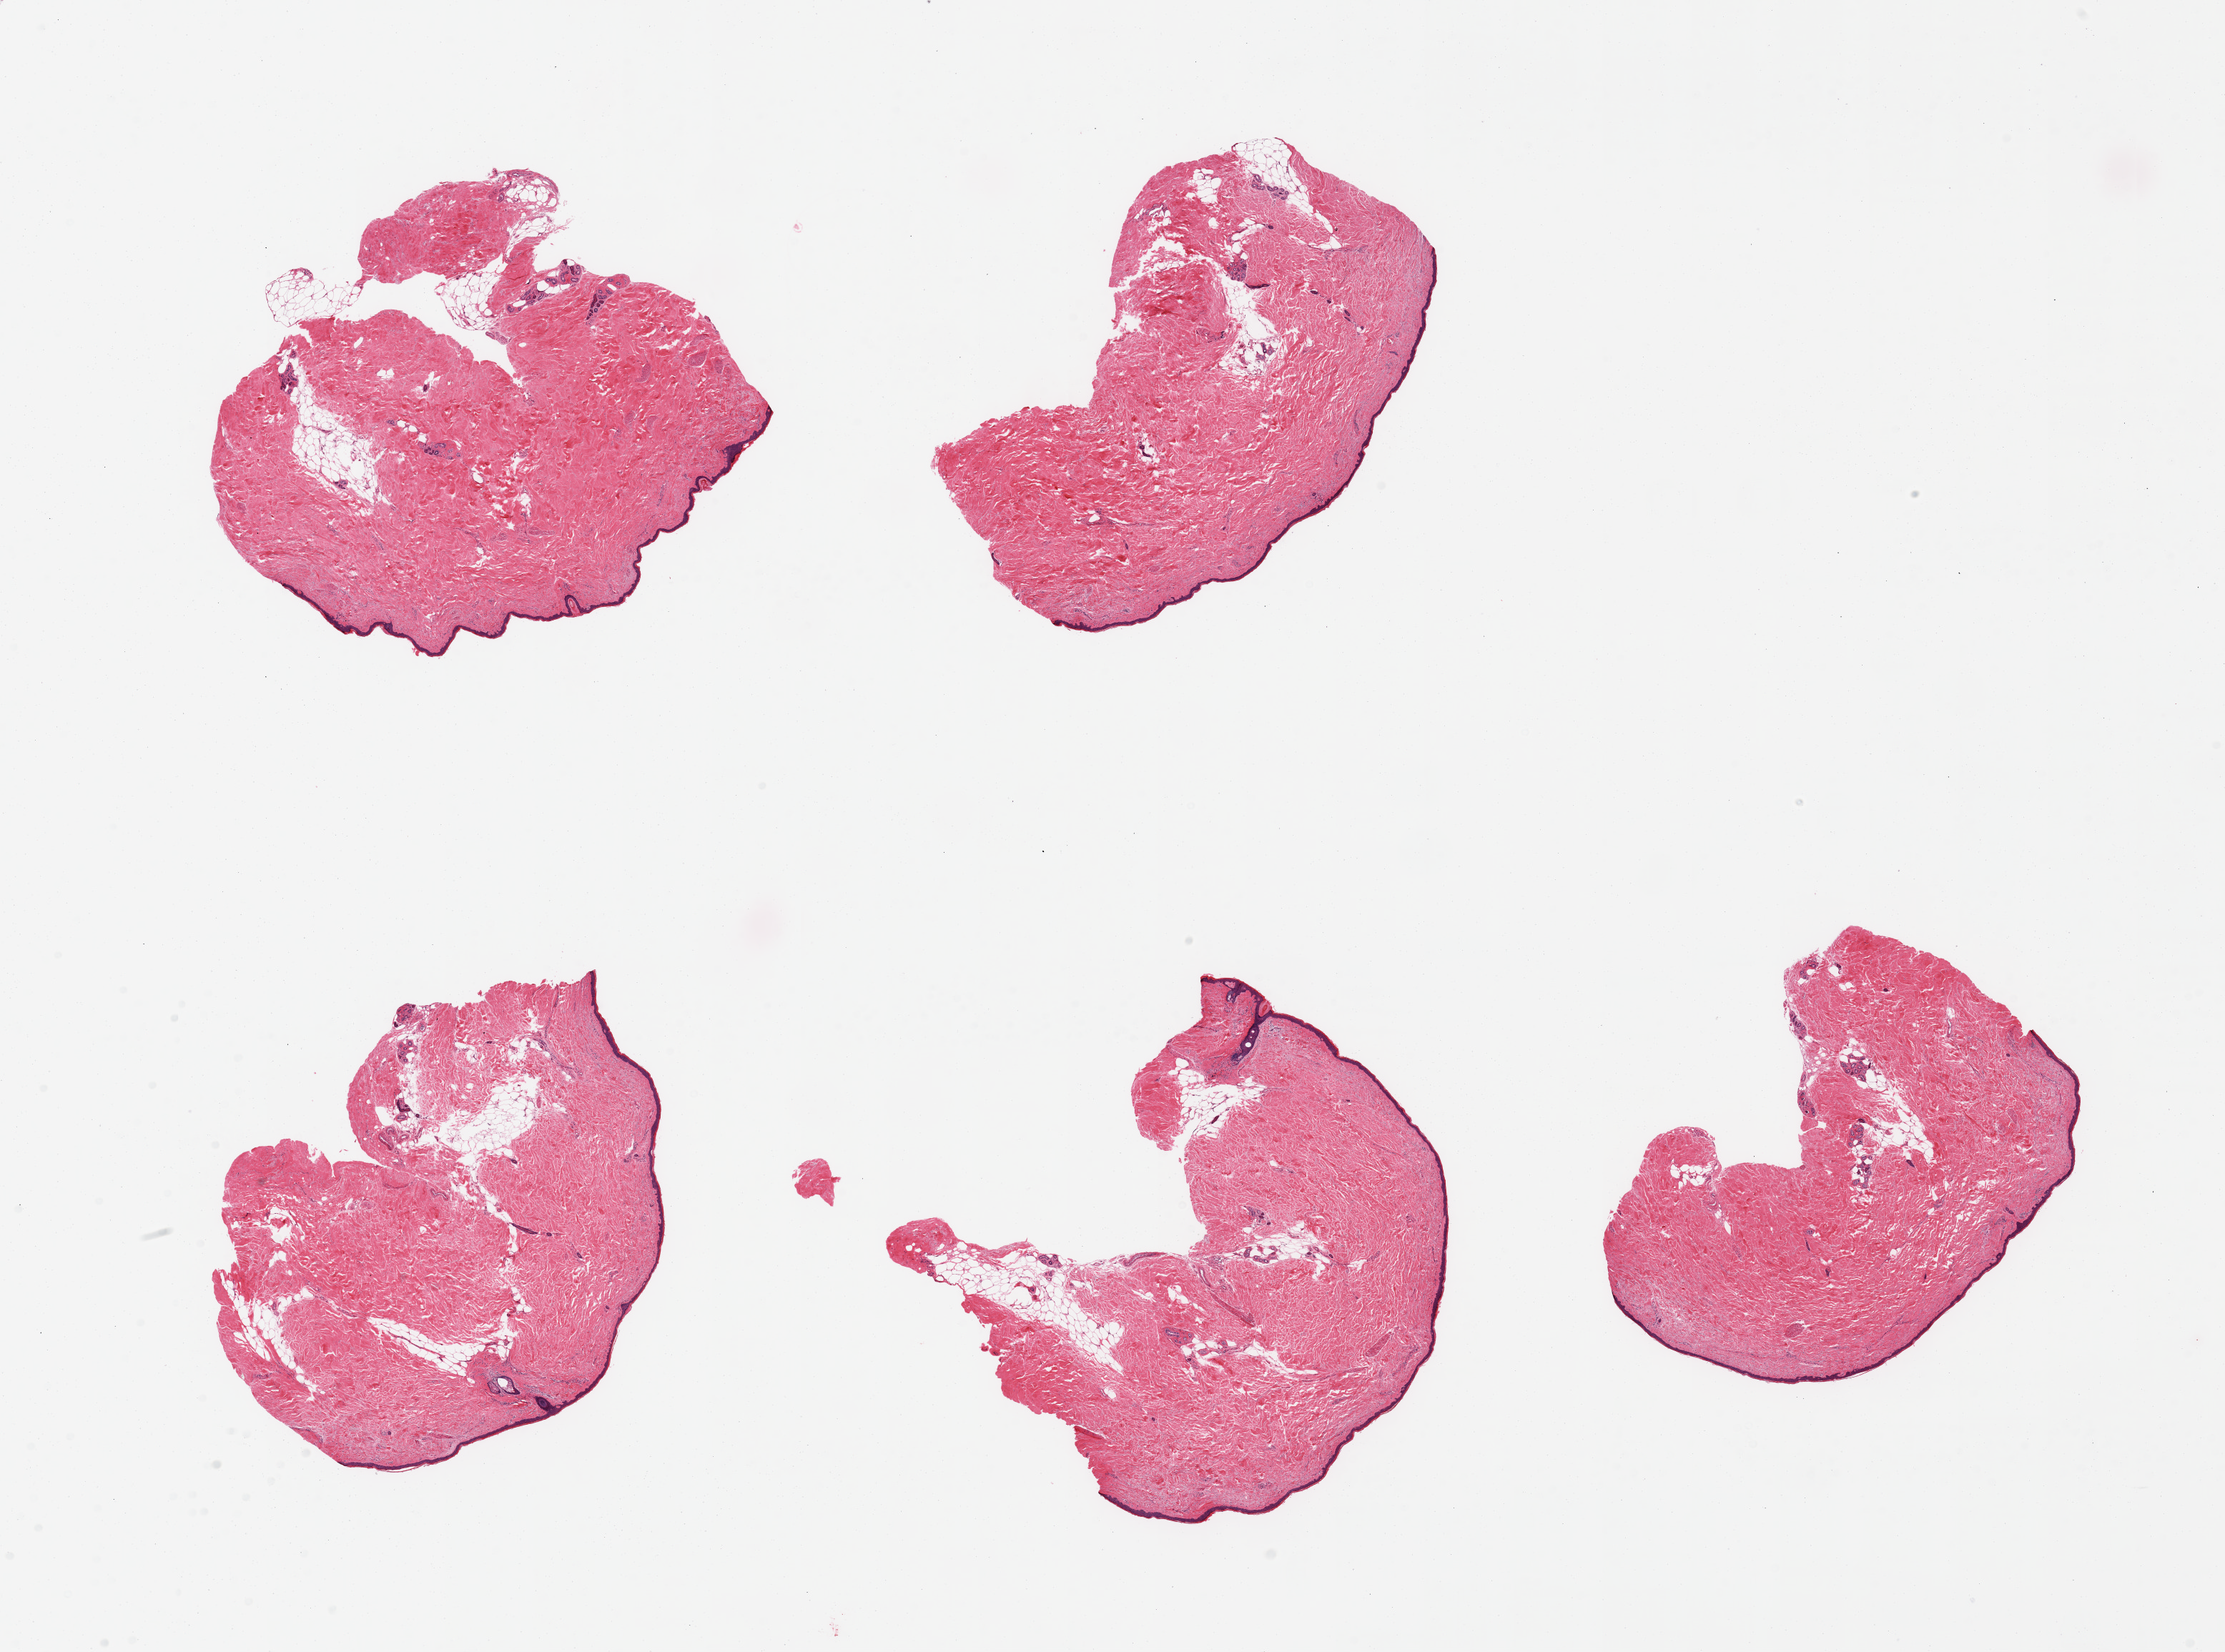
Hematoxylin and eosin (H&E) whole-slide image, brightfield — a low-resolution overview of the entire scanned area, about 24.6 x 18.3 mm (from a 20x scan), PAXgene-fixed, paraffin-embedded tissue, target tissue: skin of lower leg, donor tissue sample. Donor: male.
Pathologist's review note for this sample: 5 pieces, moderate dermal fat; squamous epithelium is ~30-35 microns.